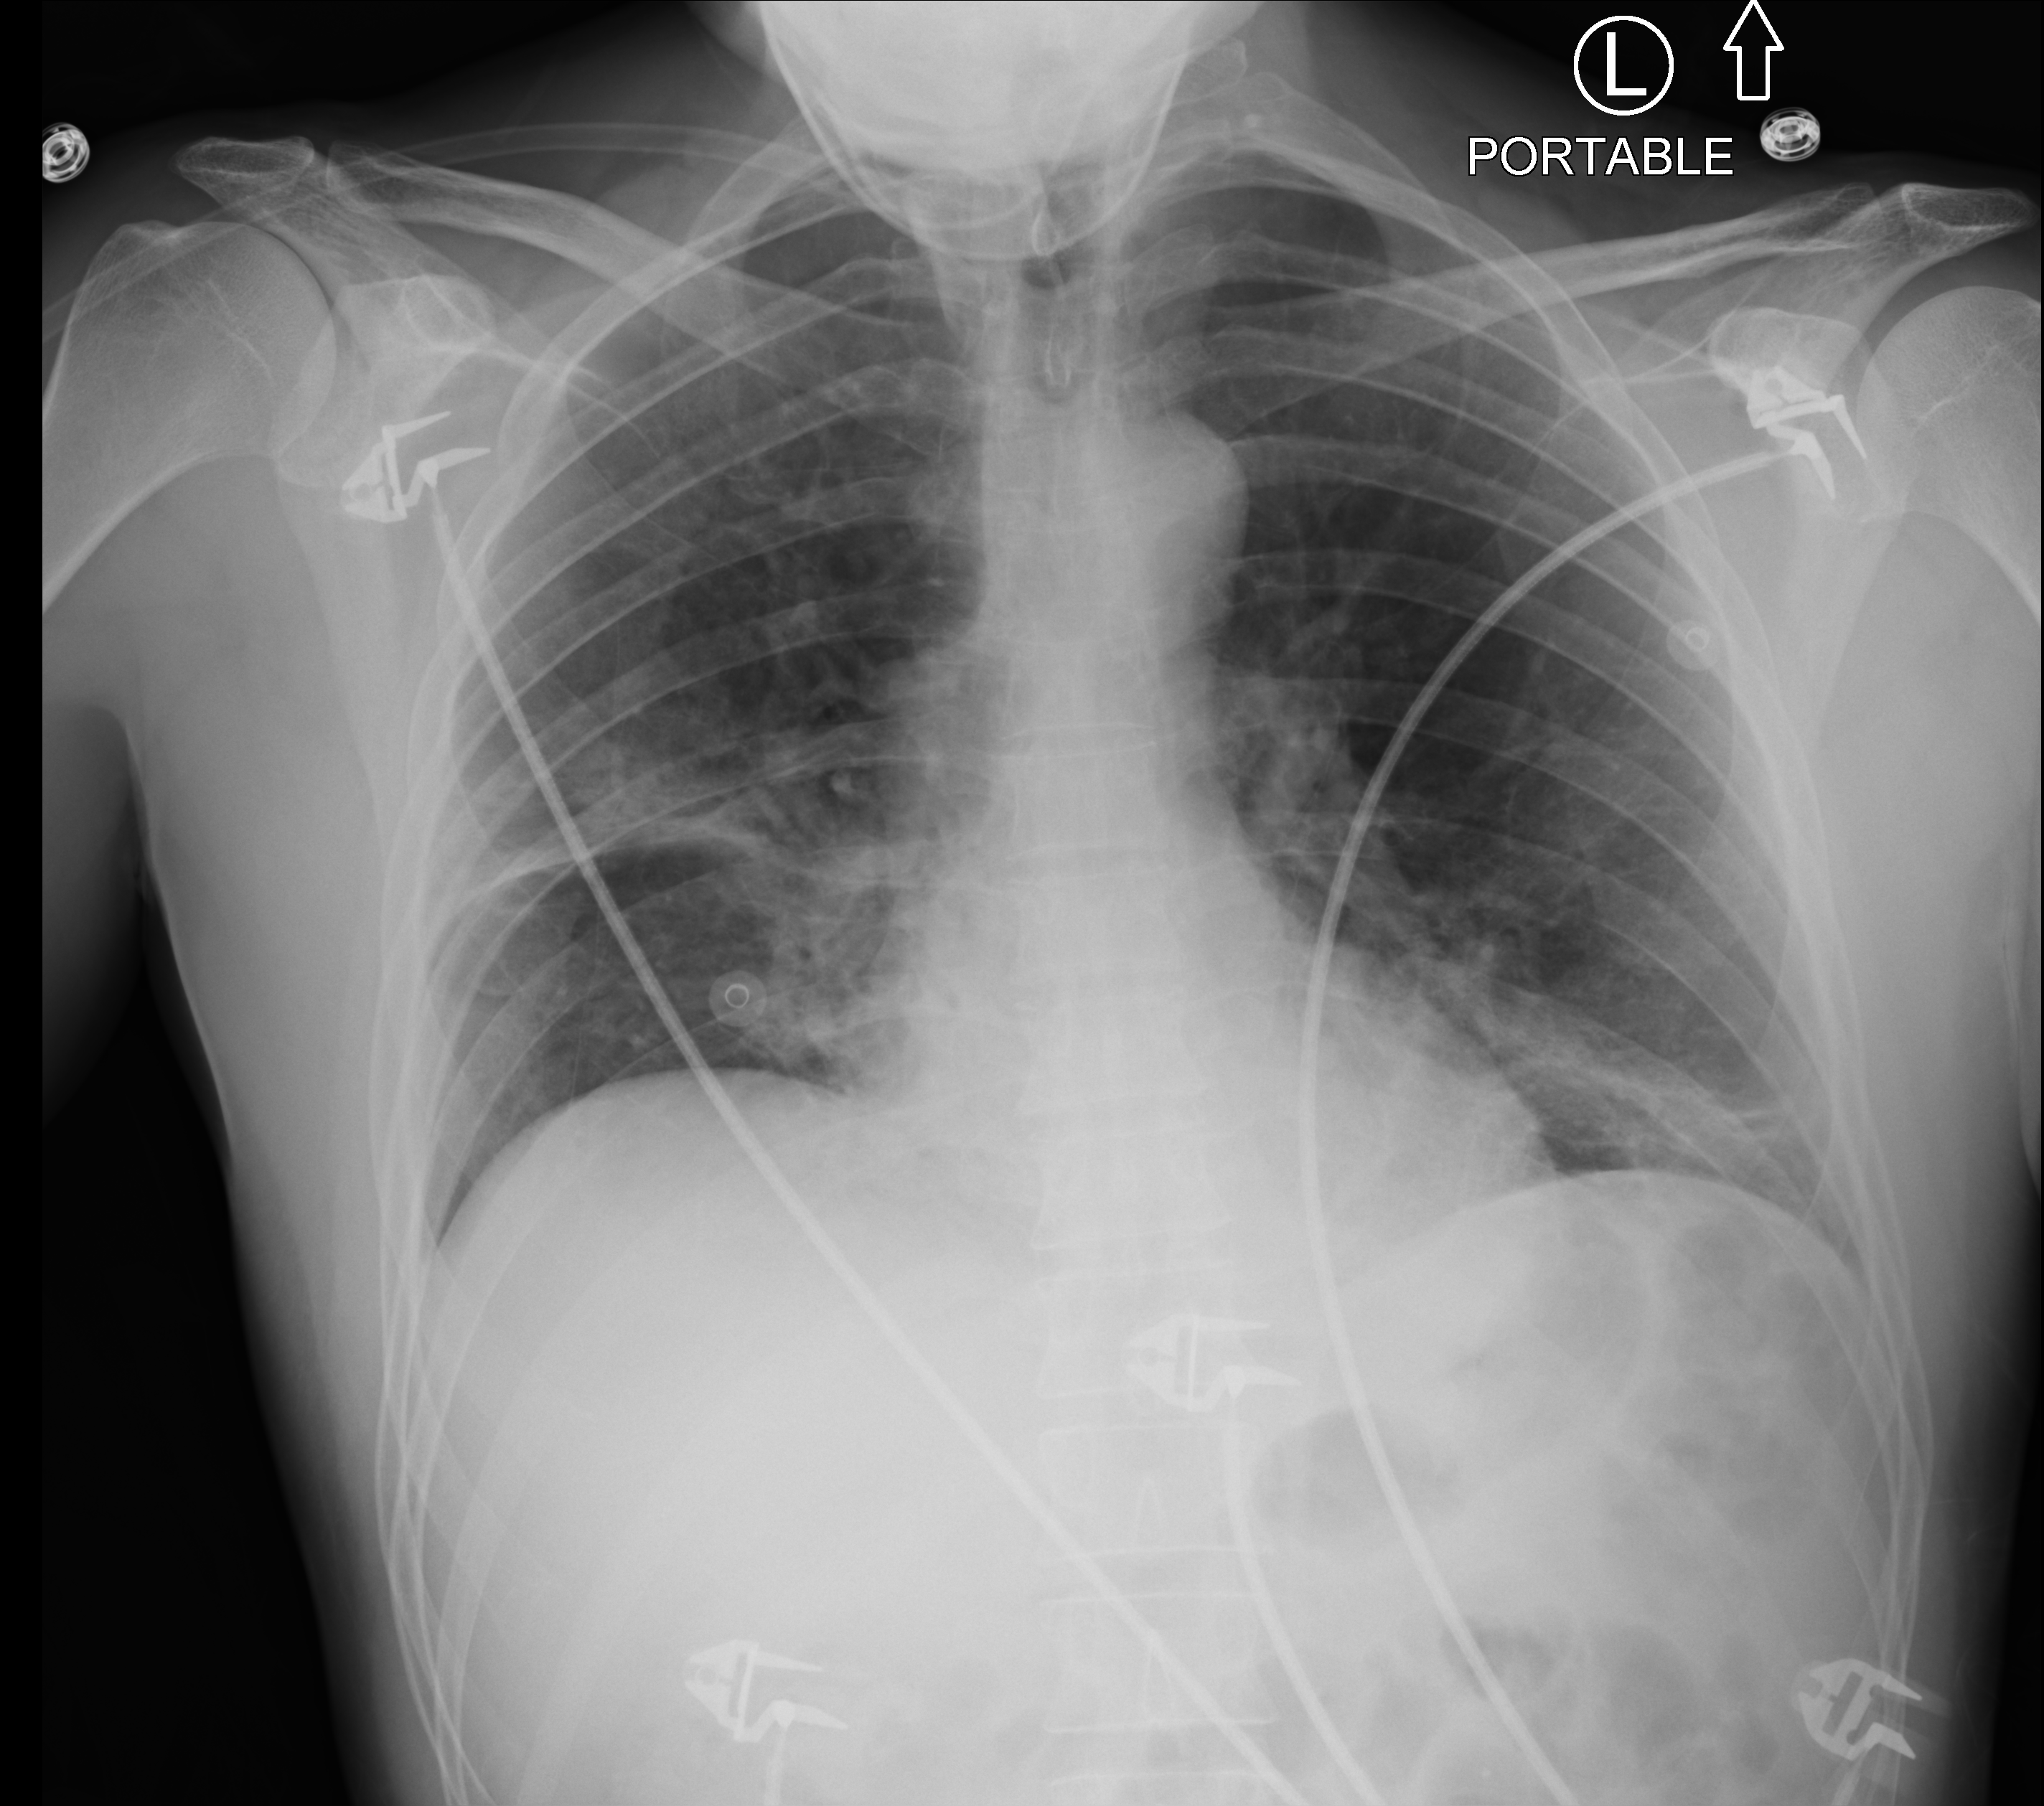
Chest X-ray (portable), anteroposterior (AP) projection. Male patient hospitalised with COVID-19, age 18–59 years.
Admission-level facts for this patient (not findings on this image; timing relative to this image not recorded): chronic kidney disease (admission record): no.